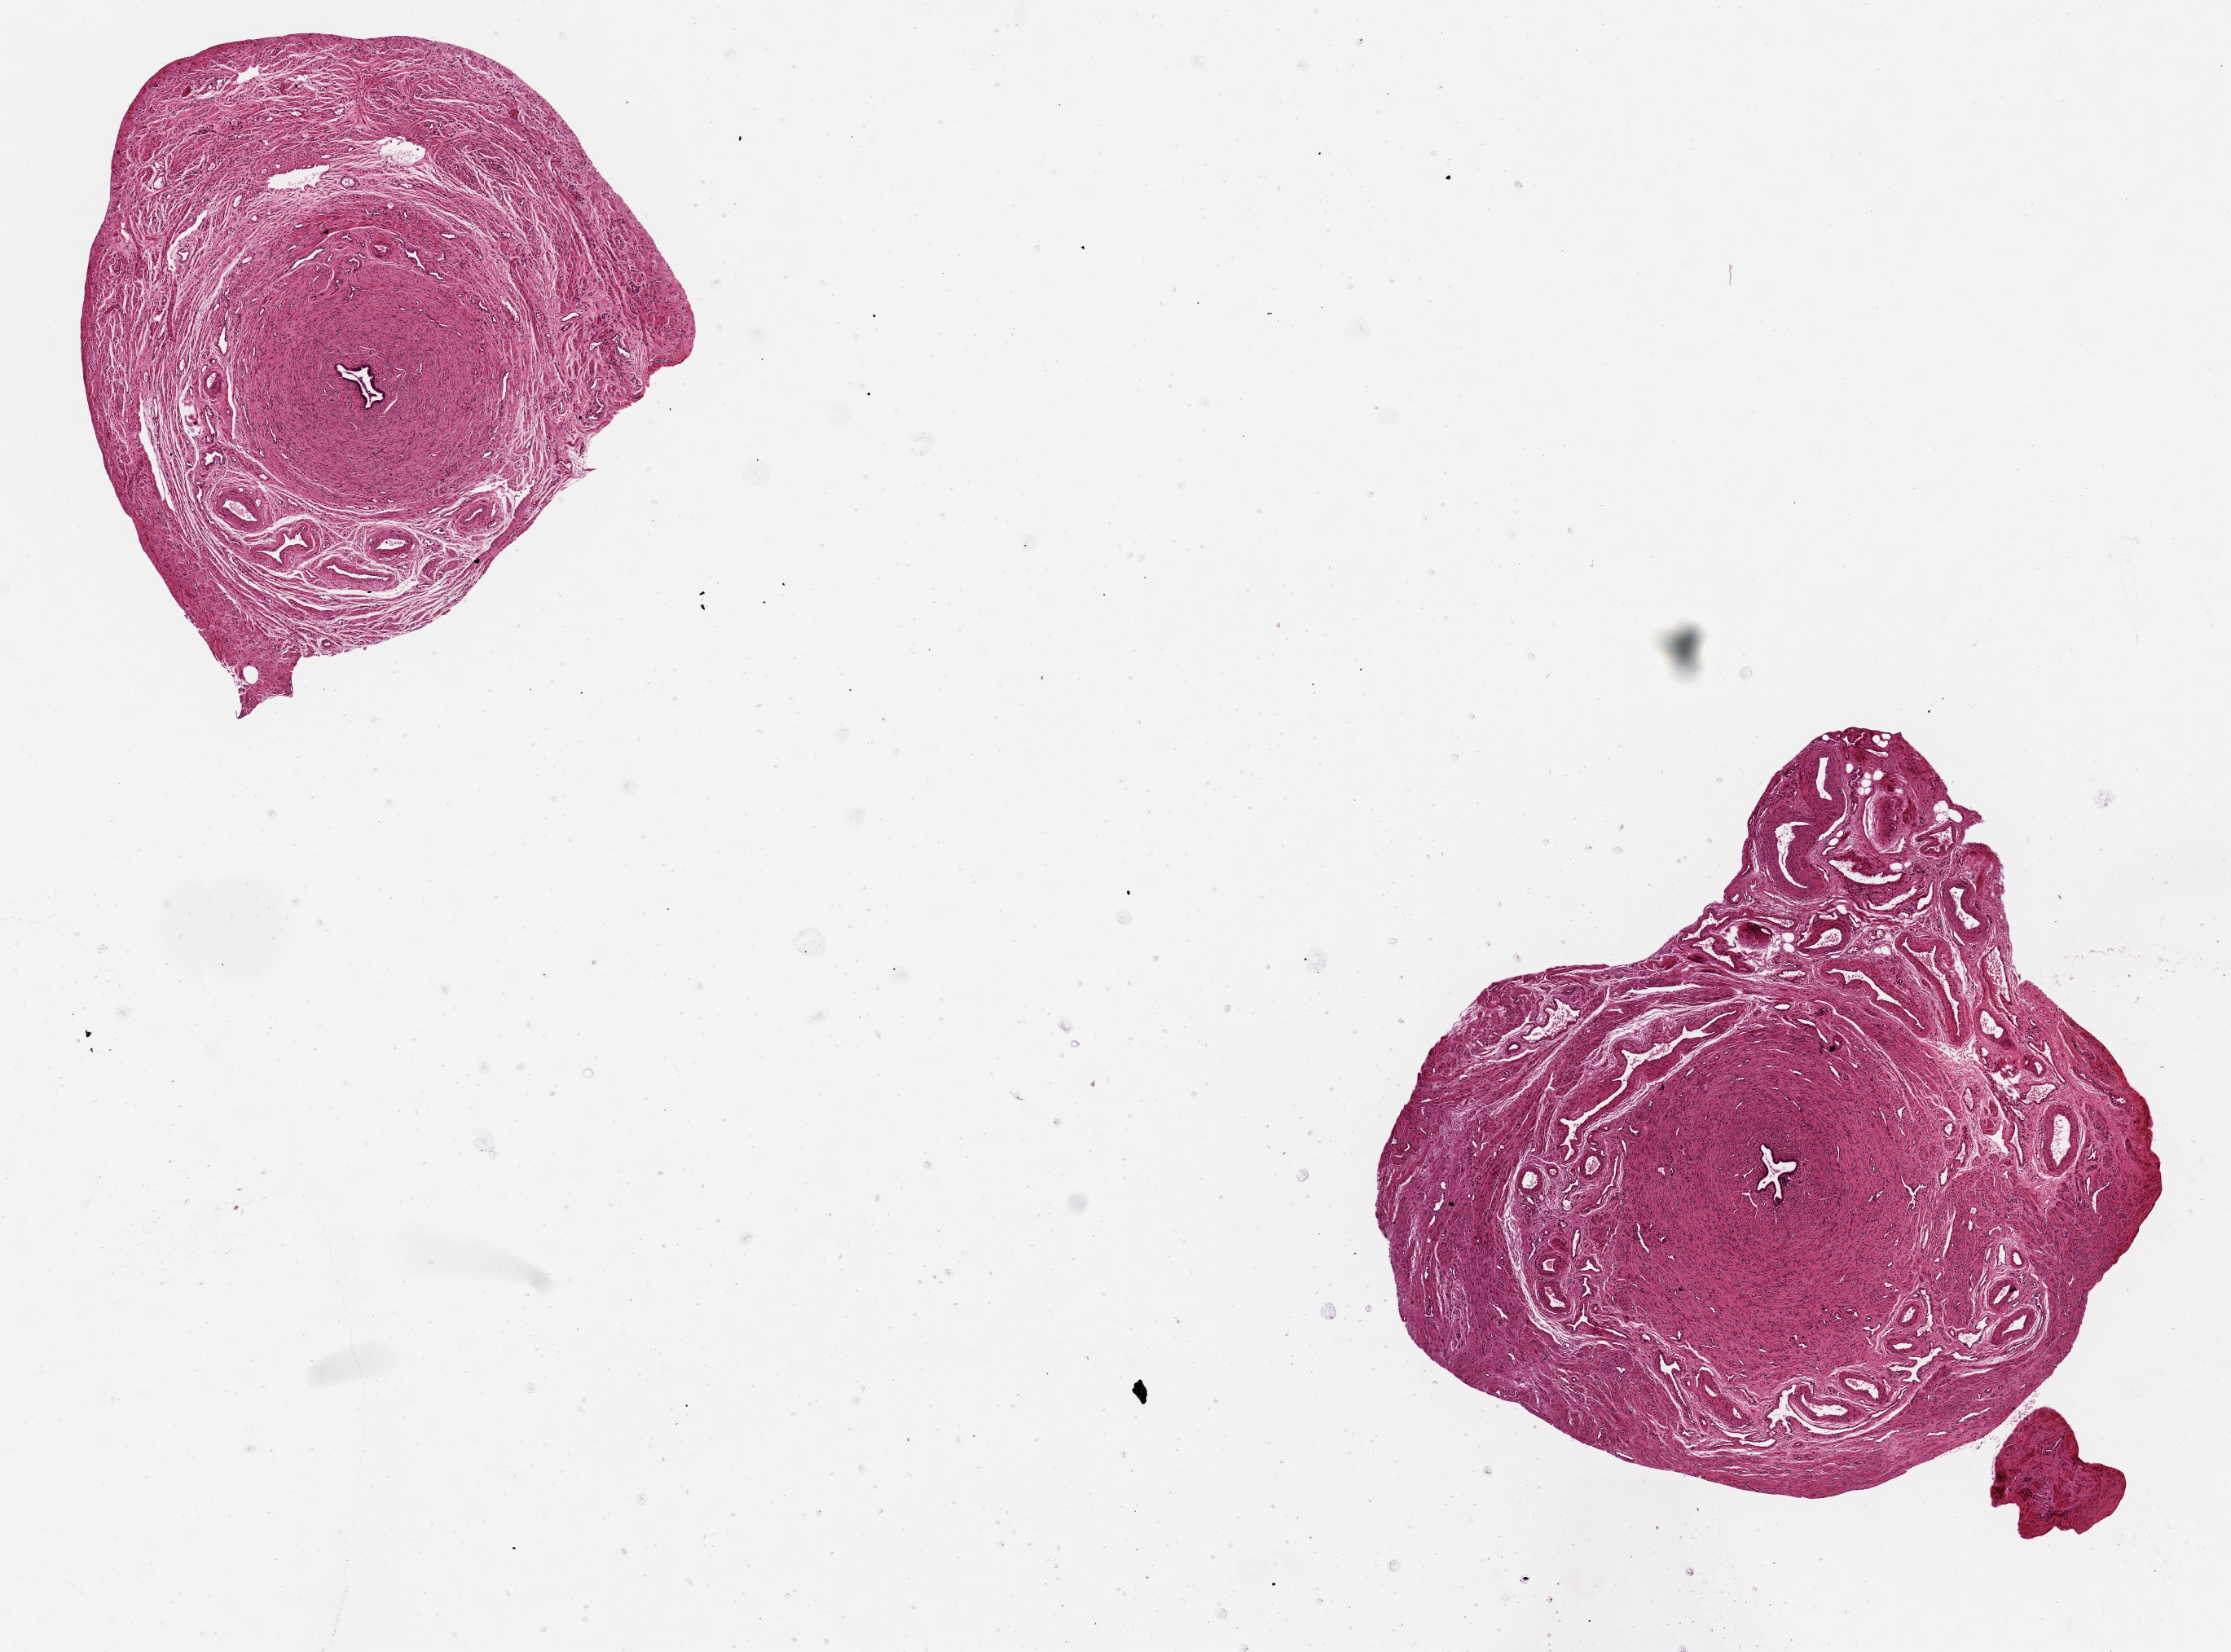
Whole-slide image, hematoxylin and eosin (H&E) stain, shown as a low-resolution overview of the whole scanned area (about 10.8 x 8.0 mm, acquisition: 20x scan). PAXgene-fixed paraffin-embedded (PFPE) section. Section of fallopian tube (target tissue). Donor tissue sample. Female donor.
Review note (as recorded): 2 pieces ~2.5mm d. Lumina less than 10% of average diameter, probably proximal/infundibular origin.